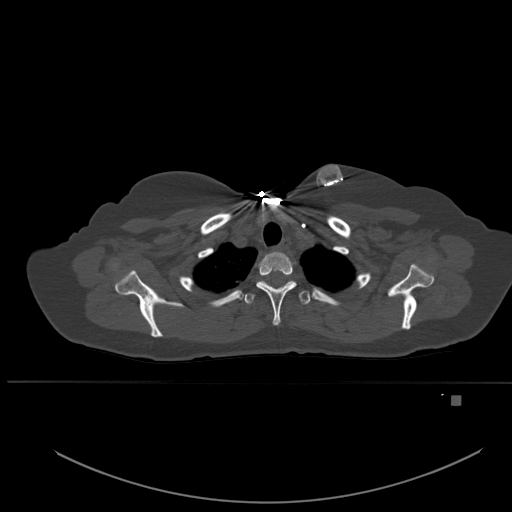
CT including the spine, one axial slice. Slice 415 of 651 in the series (ordered by position). Bone window (W 1800 / L 400 HU). 1.5 mm slice thickness. 512 × 512 image matrix, field of view 443 × 443 mm. Female patient, age 49 years. Case-level facts recorded for this patient, not image findings: primary cancer: breast.
Outlined on this slice (semi-automatically segmented with operator editing):
- T1 vertebra: bounding box [x1, y1, x2, y2] px = [256, 251, 297, 326]
- T2 vertebra: [244, 281, 311, 305]